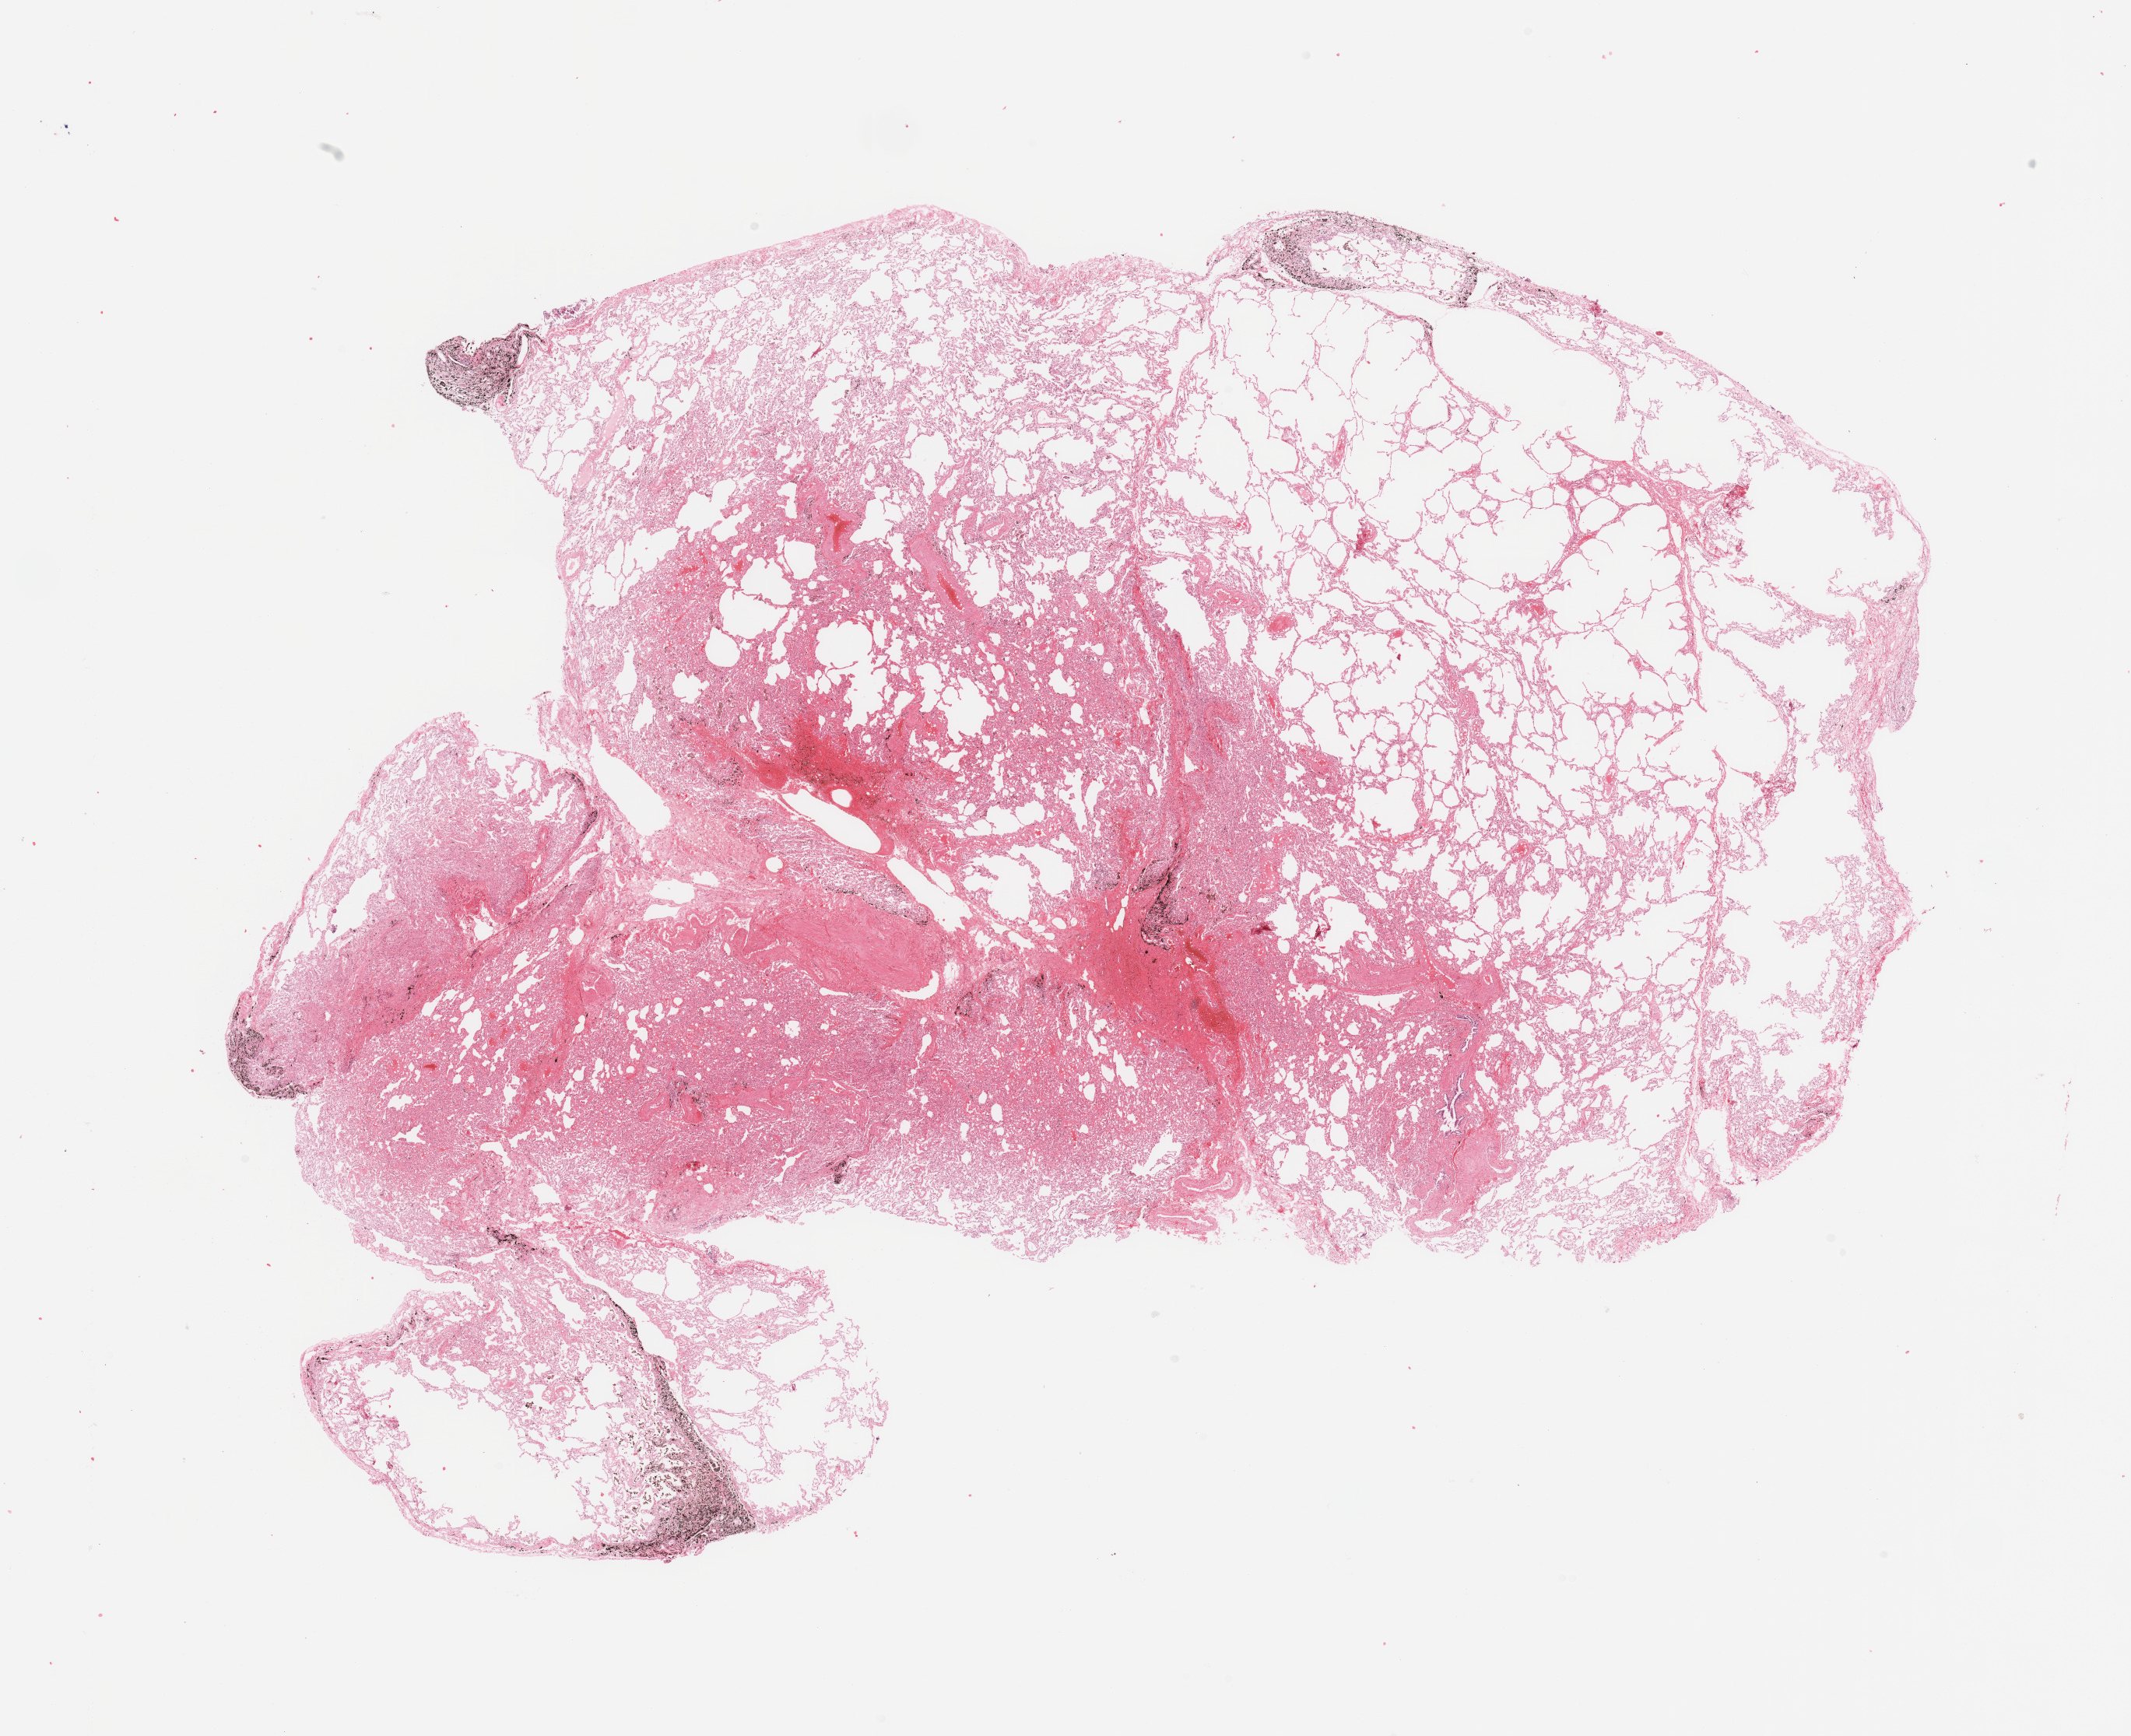
Whole-slide histology image, H&E-stained — a low-resolution overview of the entire scanned area, about 21.7 x 17.6 mm (slide scanned at 20x), normal (non-tumour) tissue sample, sampled site: lung. Patient: male, age 62 years.
This section: normal (non-tumour) tissue from the same patient. Patient diagnosis: Adenocarcinoma, NOS.